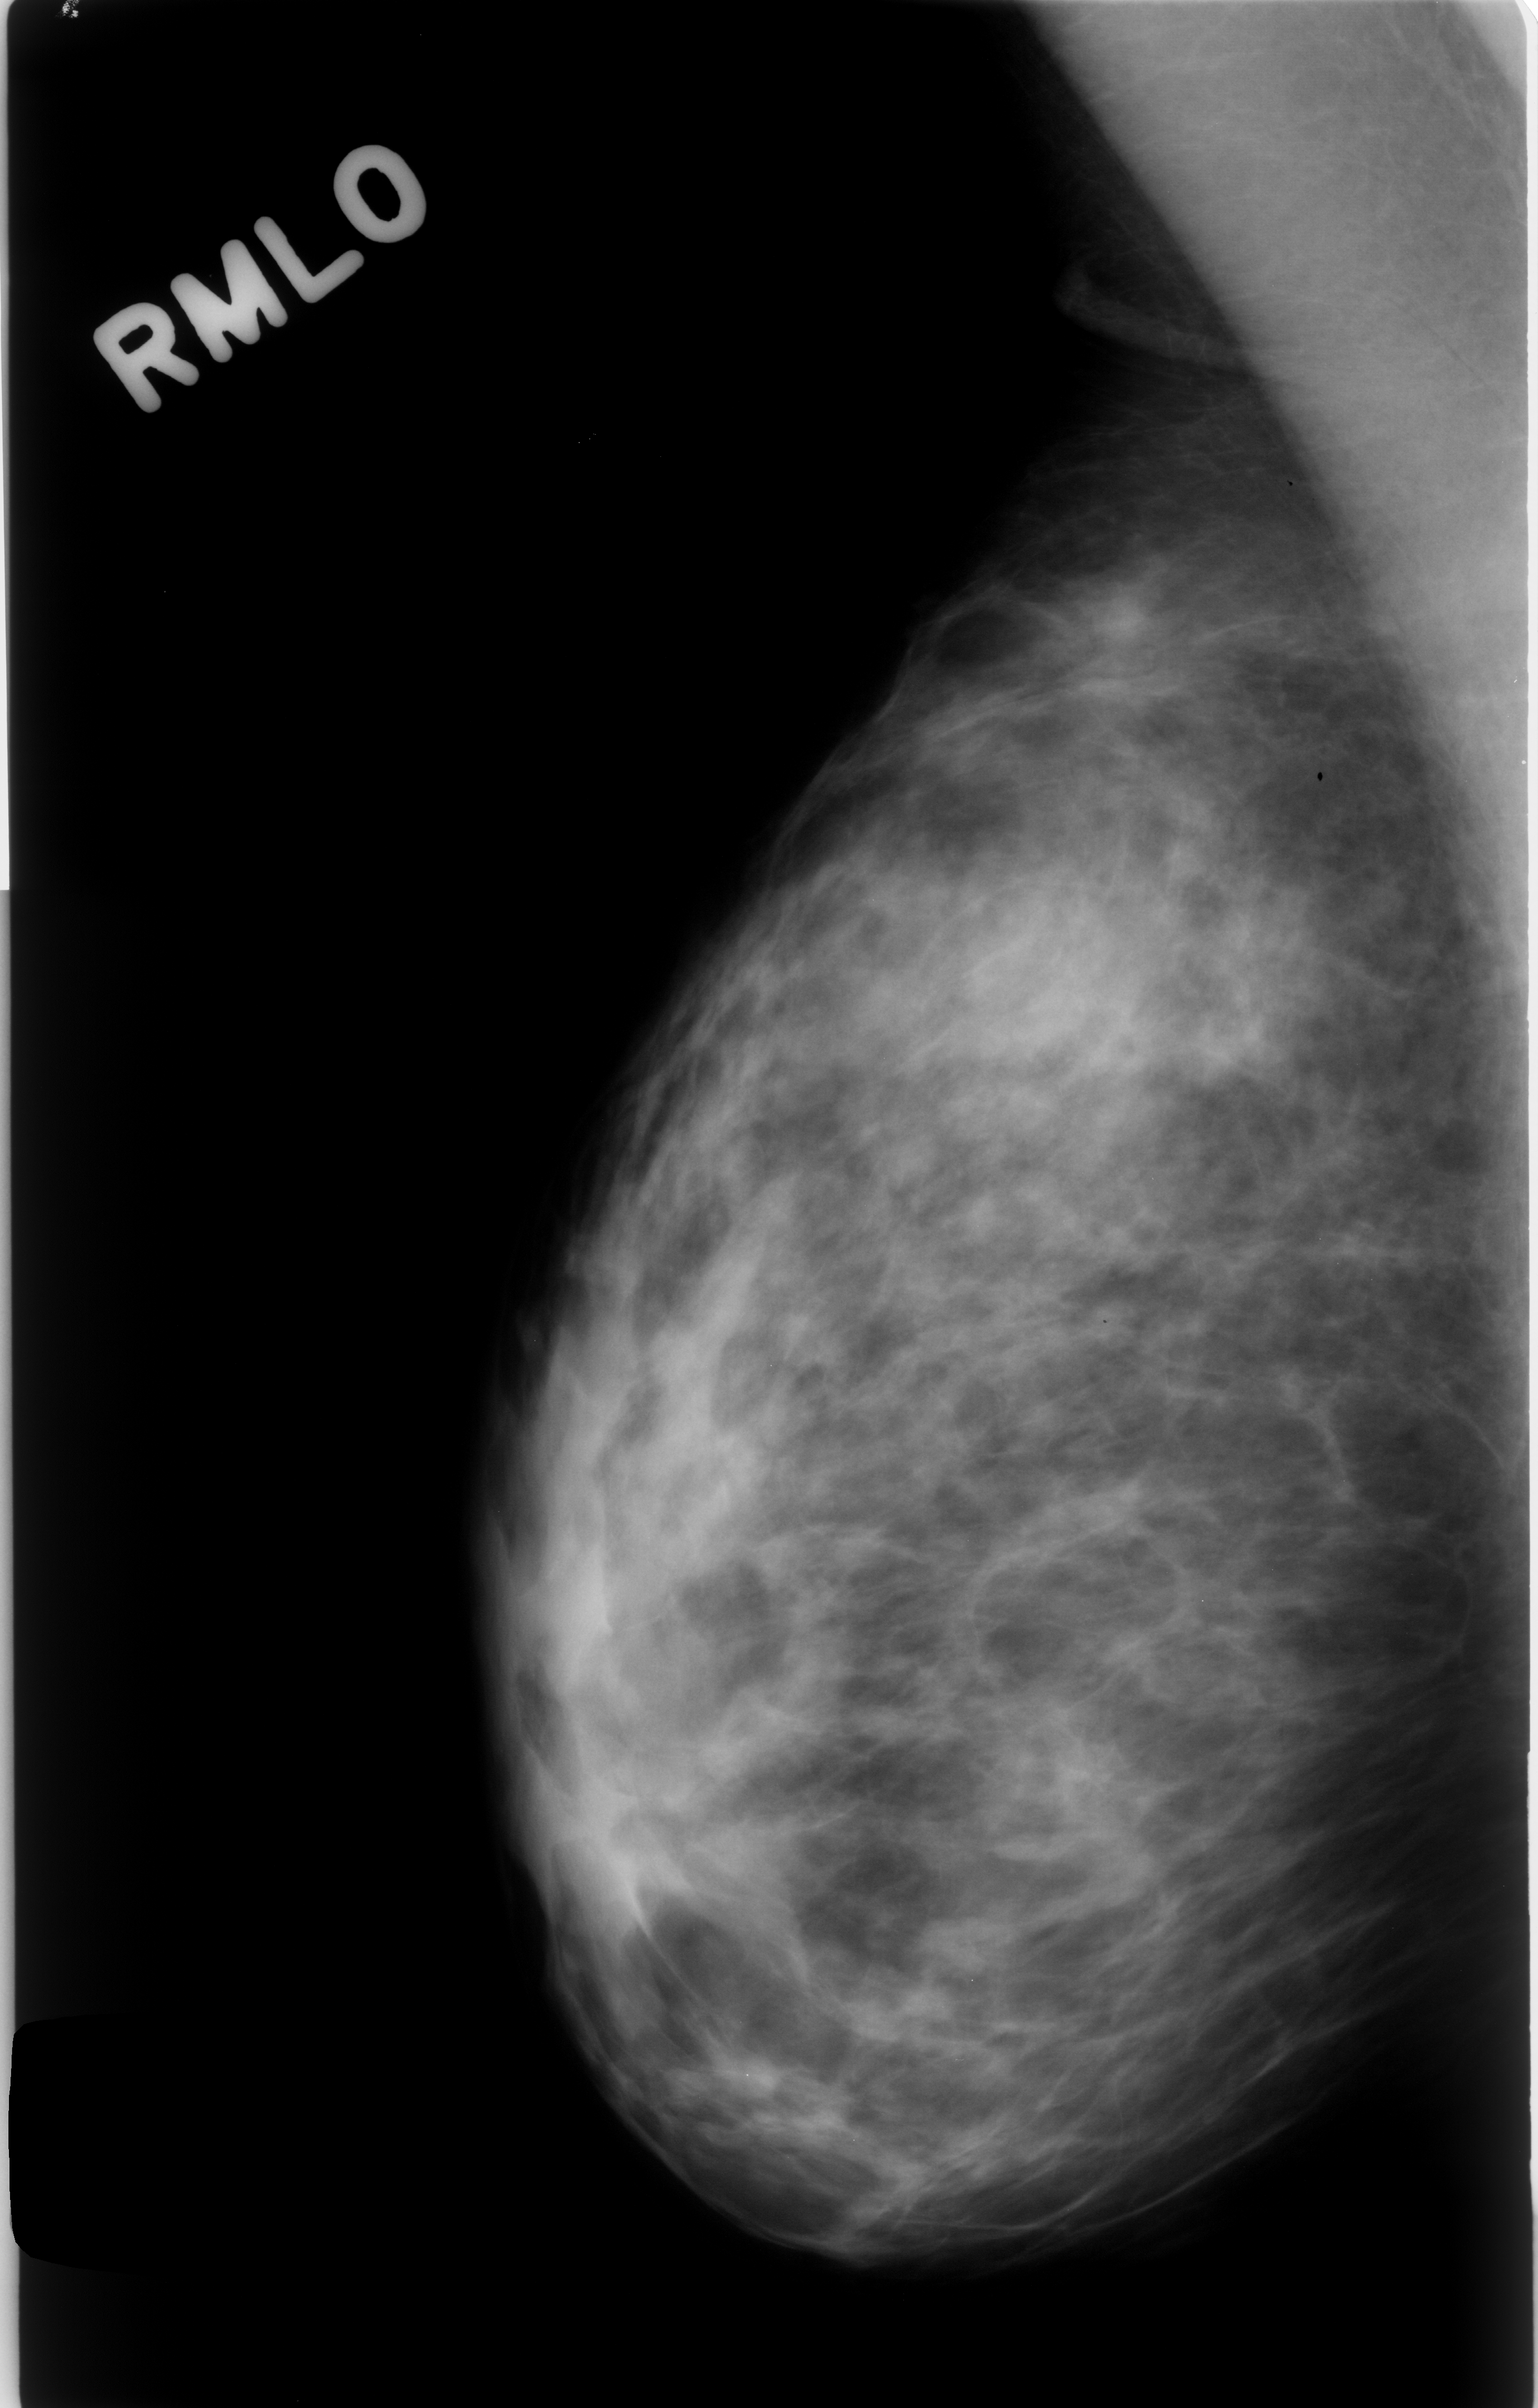
Scanned film-screen mammogram, right breast, MLO view, BI-RADS breast density category 2 (scale 1–4).
Abnormality record for this image: mass, shape architectural distortion, margins spiculated; BI-RADS assessment category 4; subtlety rating 5 on a 1 (subtle) to 5 (obvious) scale; benign; no additional work-up was recommended (benign without callback).